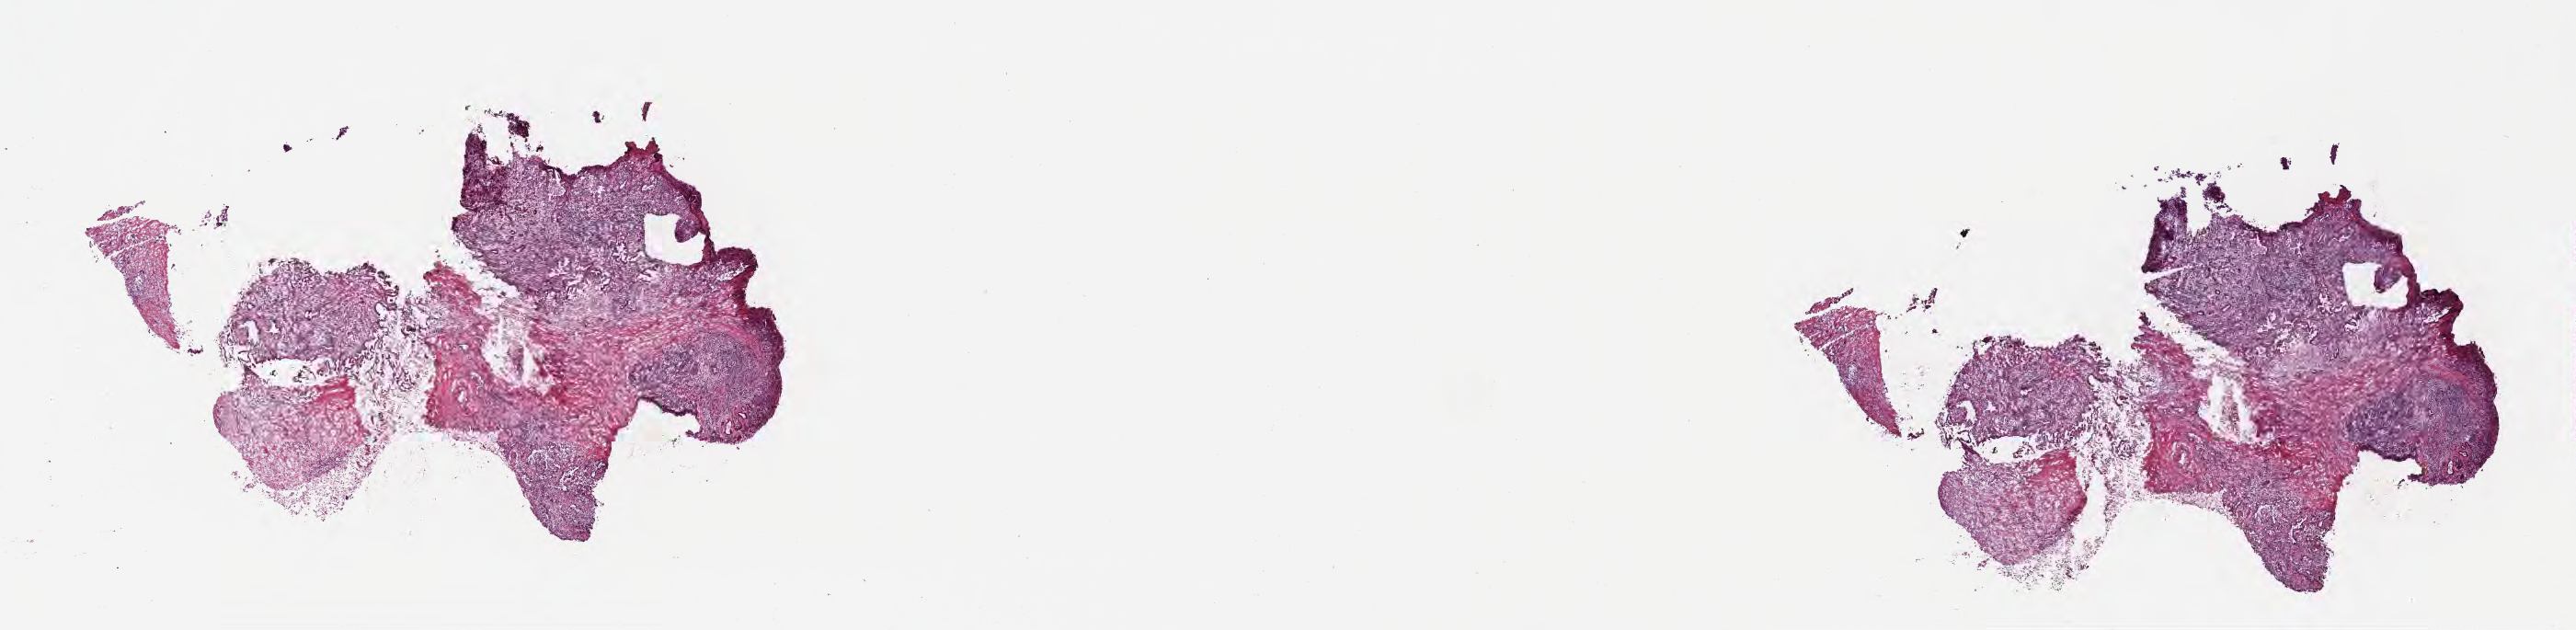
Whole-slide image, haematoxylin and eosin stain, shown as a low-resolution overview of the whole scanned area (about 22.6 x 5.5 mm), frozen section (tissue freezing medium), primary tumor, anatomic site: head of pancreas. Patient: male, age at initial diagnosis 54 years. Tumor grade: G2 (moderately differentiated). Slide review estimates, as recorded: tumor cells 20%, tumor nuclei 20%, stromal cells 40%, necrosis 0%, normal cells 40%. Infiltration values recorded for this section: lymphocyte infiltration 25%, monocyte infiltration 5%, neutrophil infiltration 2%.
AJCC pathologic stage: Stage III. Section: top of the tissue portion. Histologic diagnosis: Infiltrating duct carcinoma, NOS.